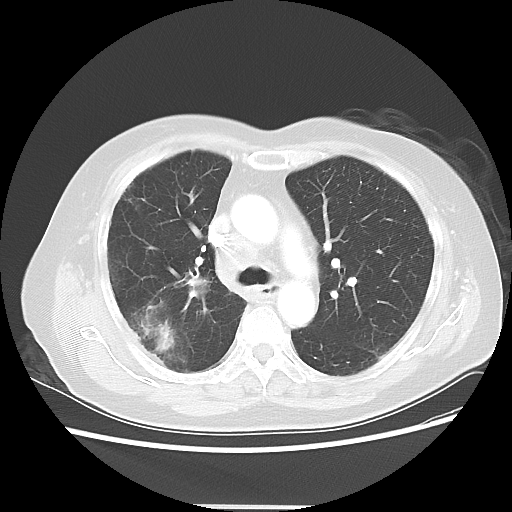
Chest CT, one axial slice; reconstruction kernel LUNG; 120 kVp; lung window (W 1500 / L -600 HU); 5 mm slice thickness; 512 × 512 image matrix. Female patient, age 72 years. Case-level facts recorded for this patient, not image findings: clinical TNM (as recorded): T2 N1 M0.
Outlined on this slice (rectangle marked by the reading radiologist):
- lung tumour (recorded histology: adenocarcinoma): bounding box (x1, y1, x2, y2) in pixels: (139, 311, 184, 358)